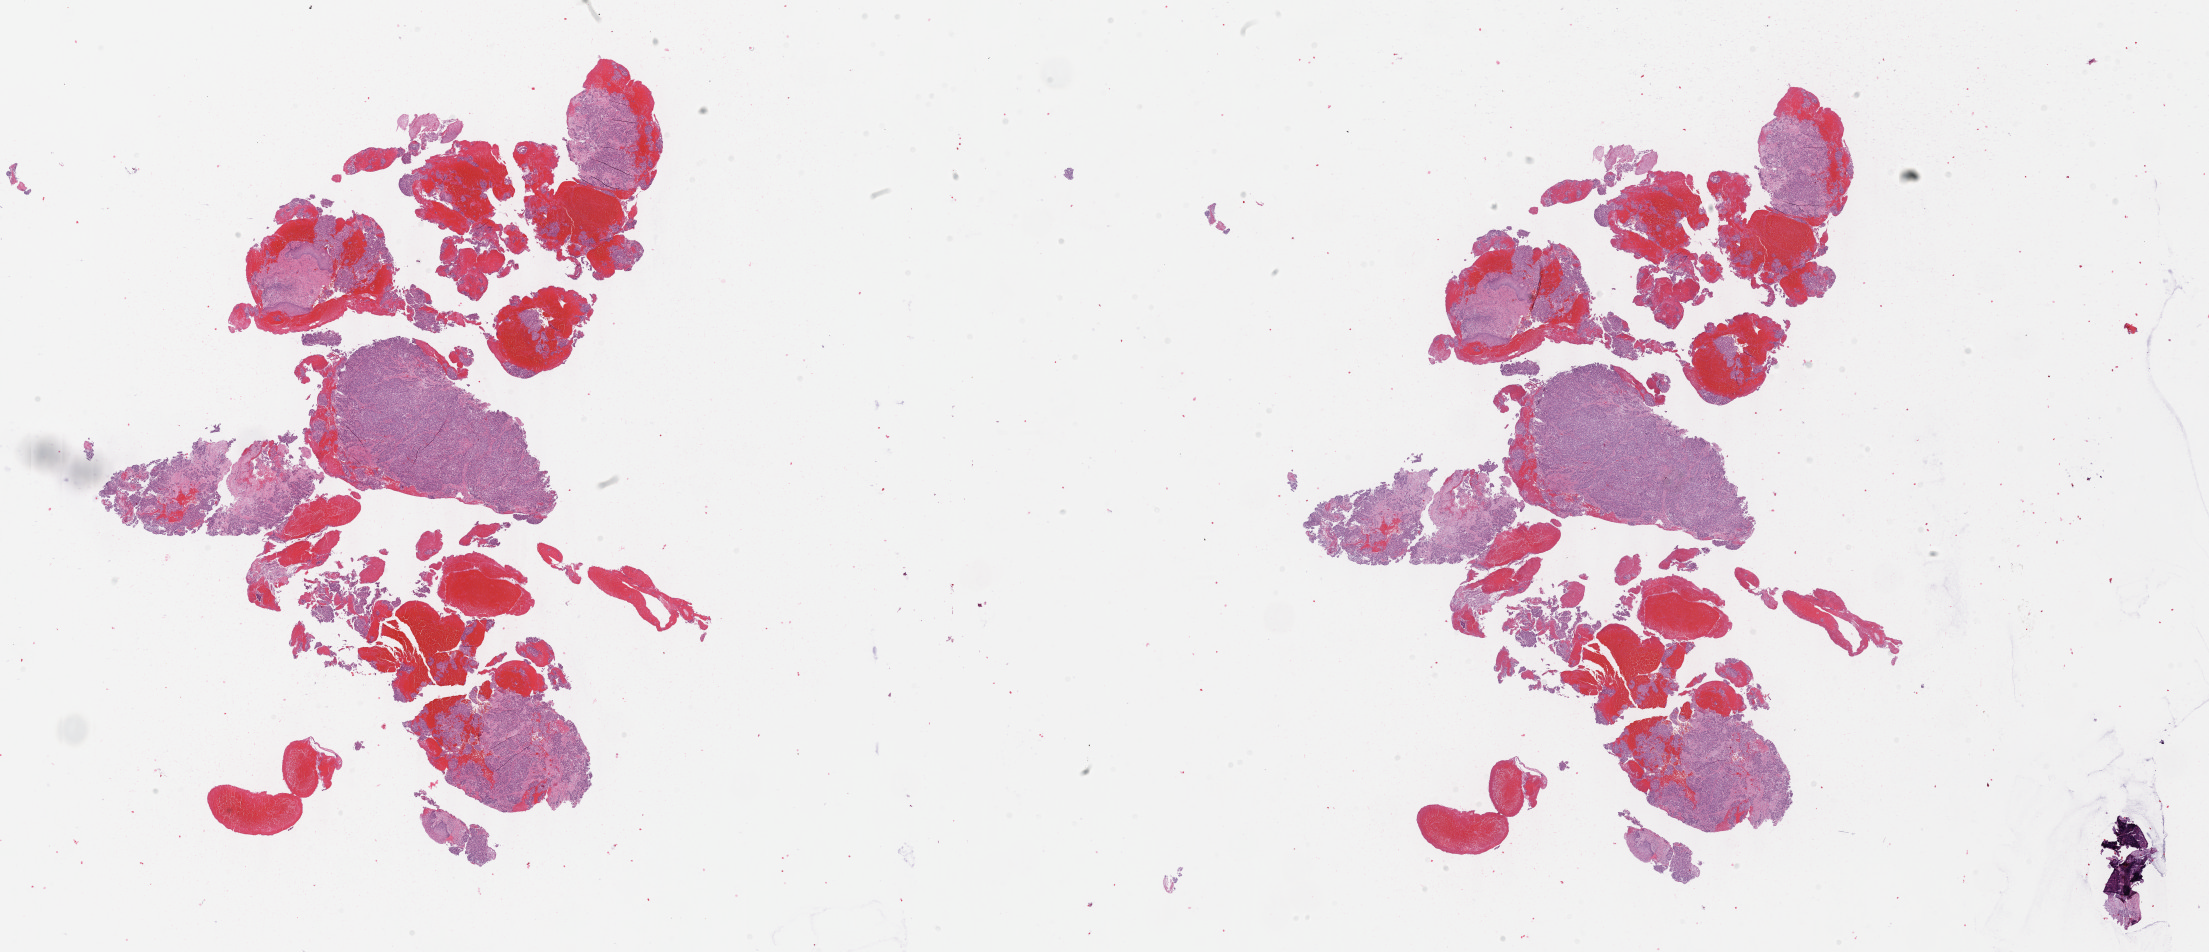
Whole-slide histology image, Hematoxylin and eosin (H&E) stained — whole scanned area (about 35.7 x 15.4 mm, slide scanned at 40x) shown as a low-resolution overview; FFPE section; sample: primary tumour, cervix. Patient: female, age at initial diagnosis 35 years. Histologic grade: G2 (moderately differentiated).
Diagnosis: Adenocarcinoma, endocervical type (cervix uteri). FIGO stage: IB2.